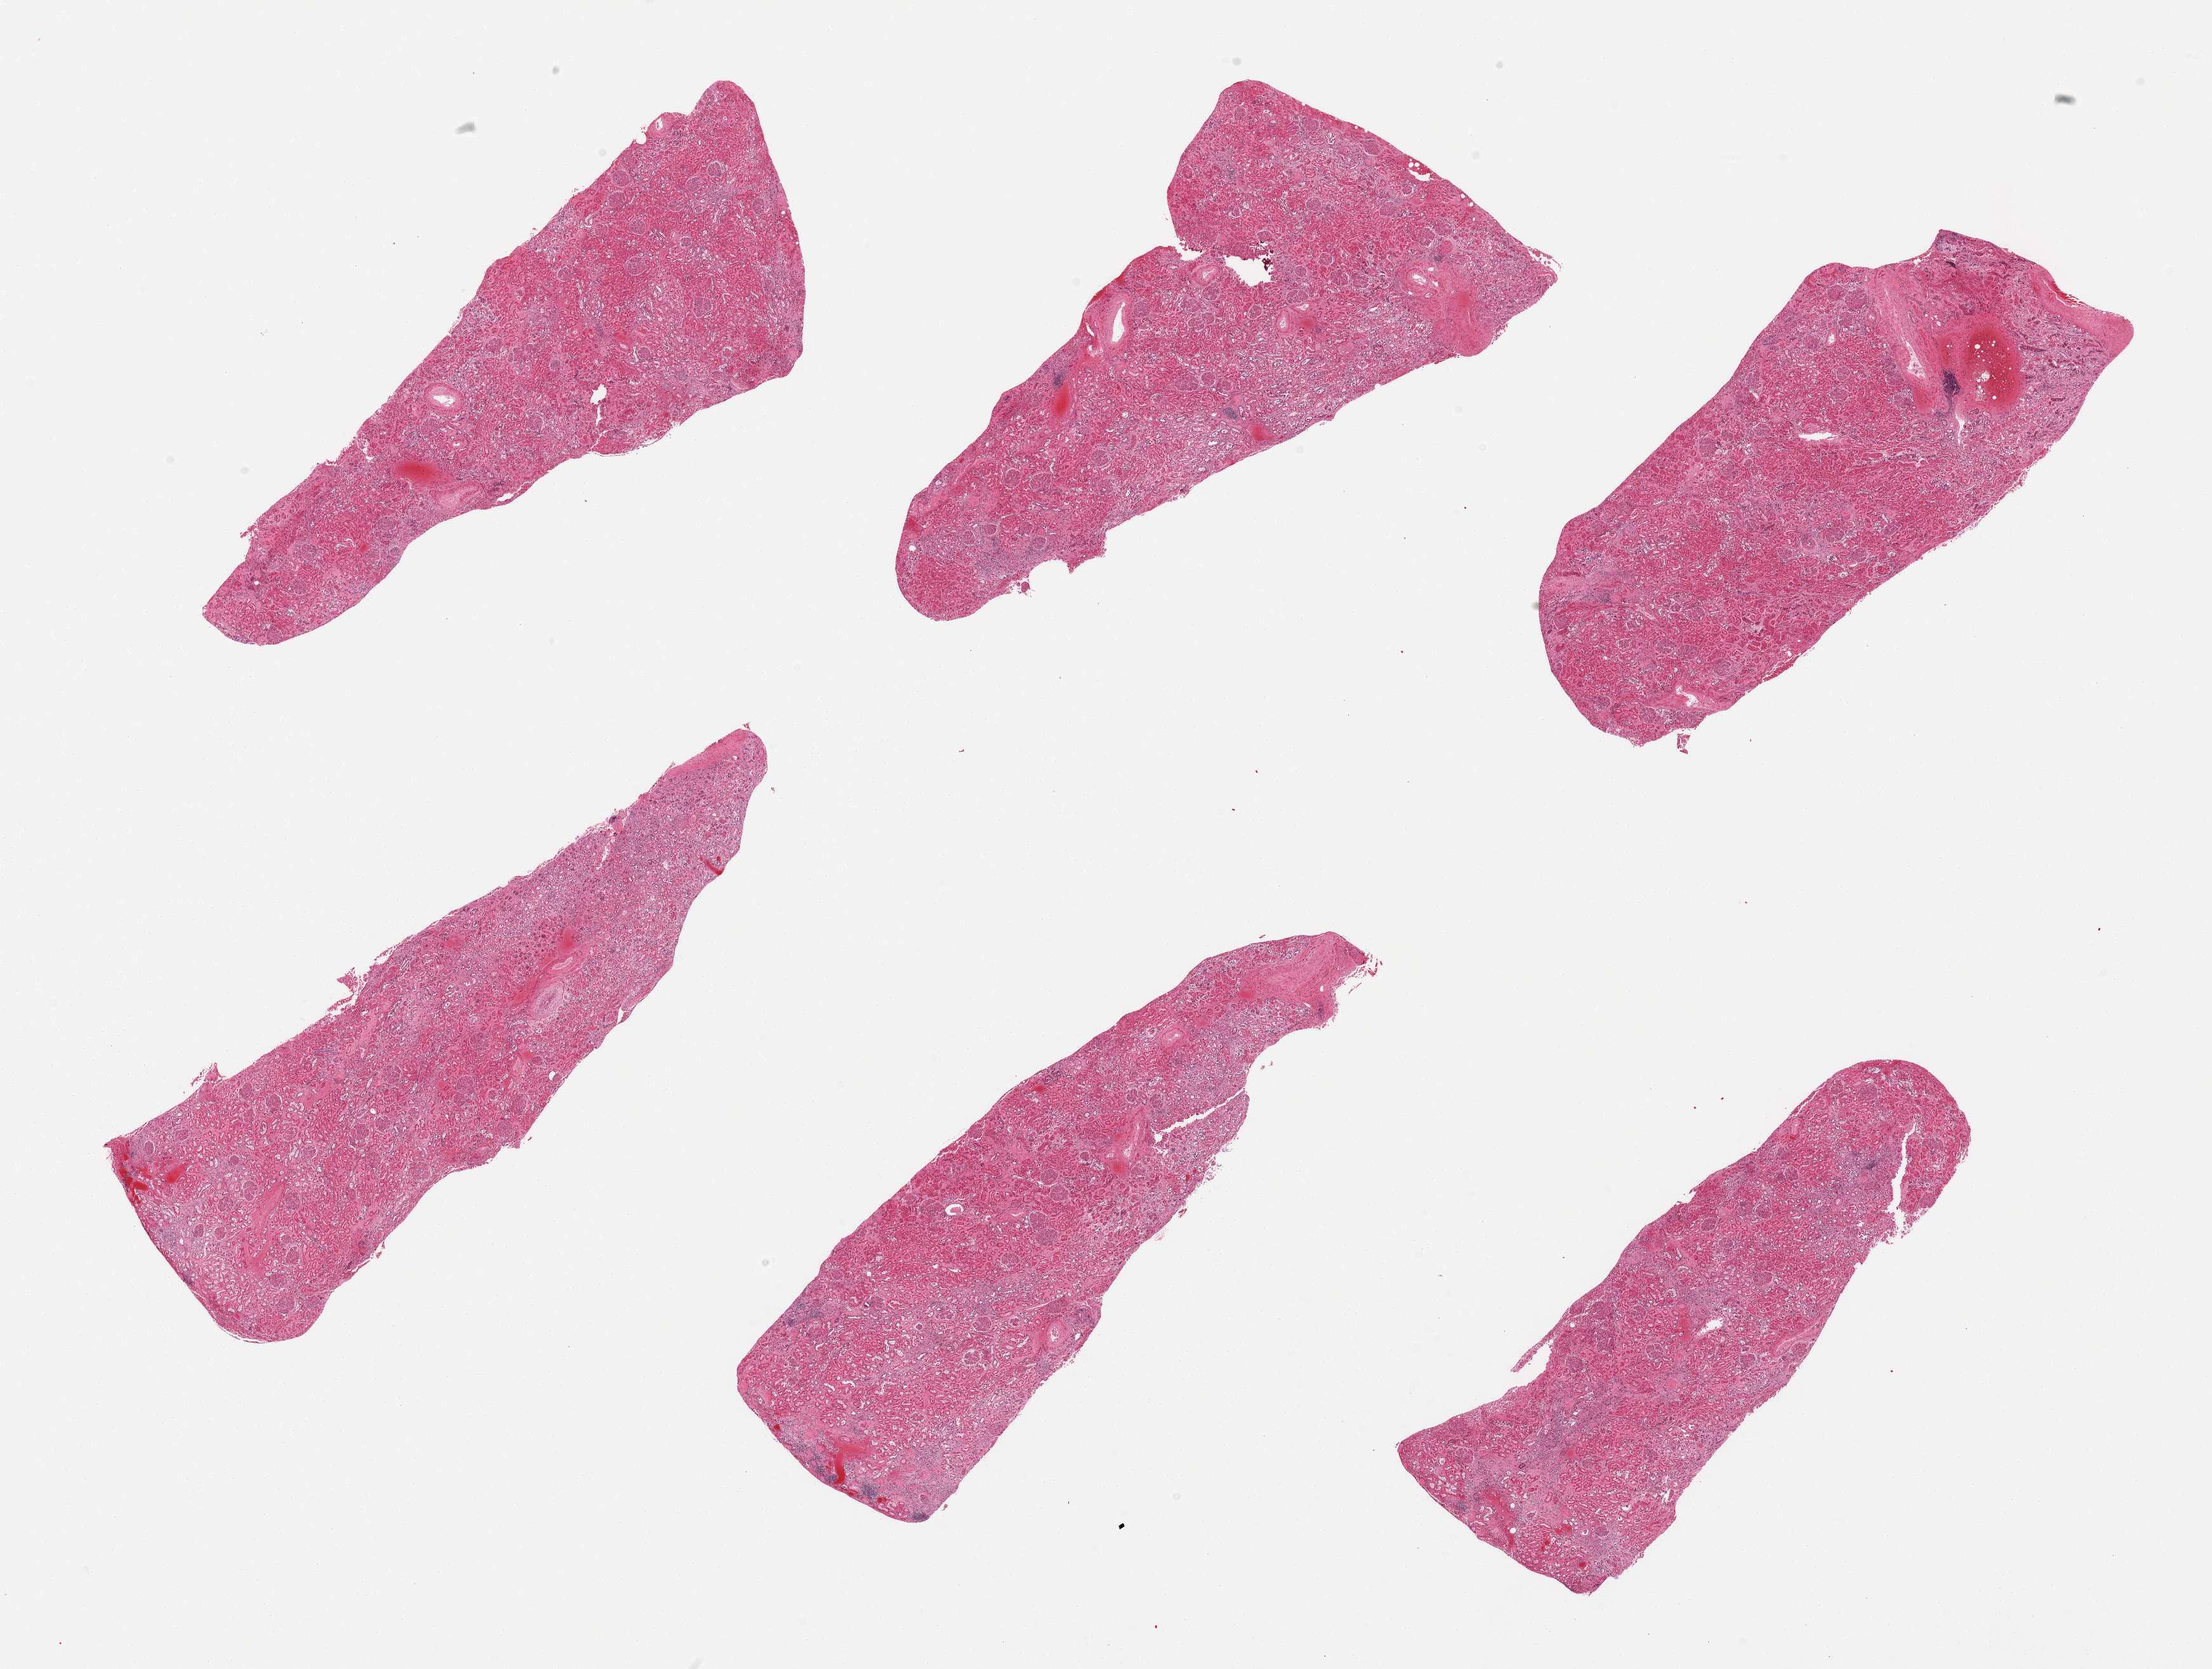
Digitized haematoxylin and eosin-stained section, brightfield — a low-resolution overview of the entire scanned area, about 27.6 x 20.8 mm; PAXgene-fixed paraffin-embedded (PFPE) section; target tissue: renal cortex; donor tissue sample. Donor sex: male.
Pathologist's review note for this sample: 6 pieces, all sections contain glomeruli, some sclerotic, pathcy chronic inflammation.